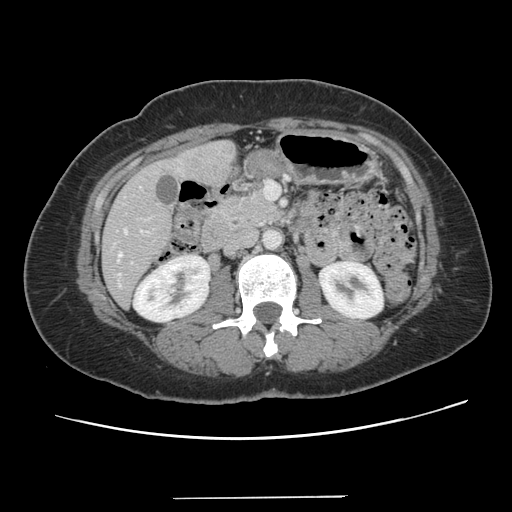
Contrast-enhanced abdominal CT, one axial slice; slice 48 of 141 in the series (ordered by position); intravenous contrast given; soft-tissue window (W 400 / L 40 HU); 2.5 mm slice thickness; 512 × 512 image matrix, field of view 366 × 366 mm. Female patient, age 53 years. From the clinical record (not read from this slice): diagnosis: colorectal cancer liver metastases, imaged before liver resection; multiple liver metastases: no; largest metastasis: 14.5 cm.
Annotated regions visible in this slice (manually delineated by an expert):
- hepatic veins: box from (x=118, y=229) to (x=126, y=258) px
- liver: (x=103, y=142)–(x=235, y=306)
- planned liver remnant (the part of the liver to remain after resection): (x=102, y=218)–(x=172, y=306)